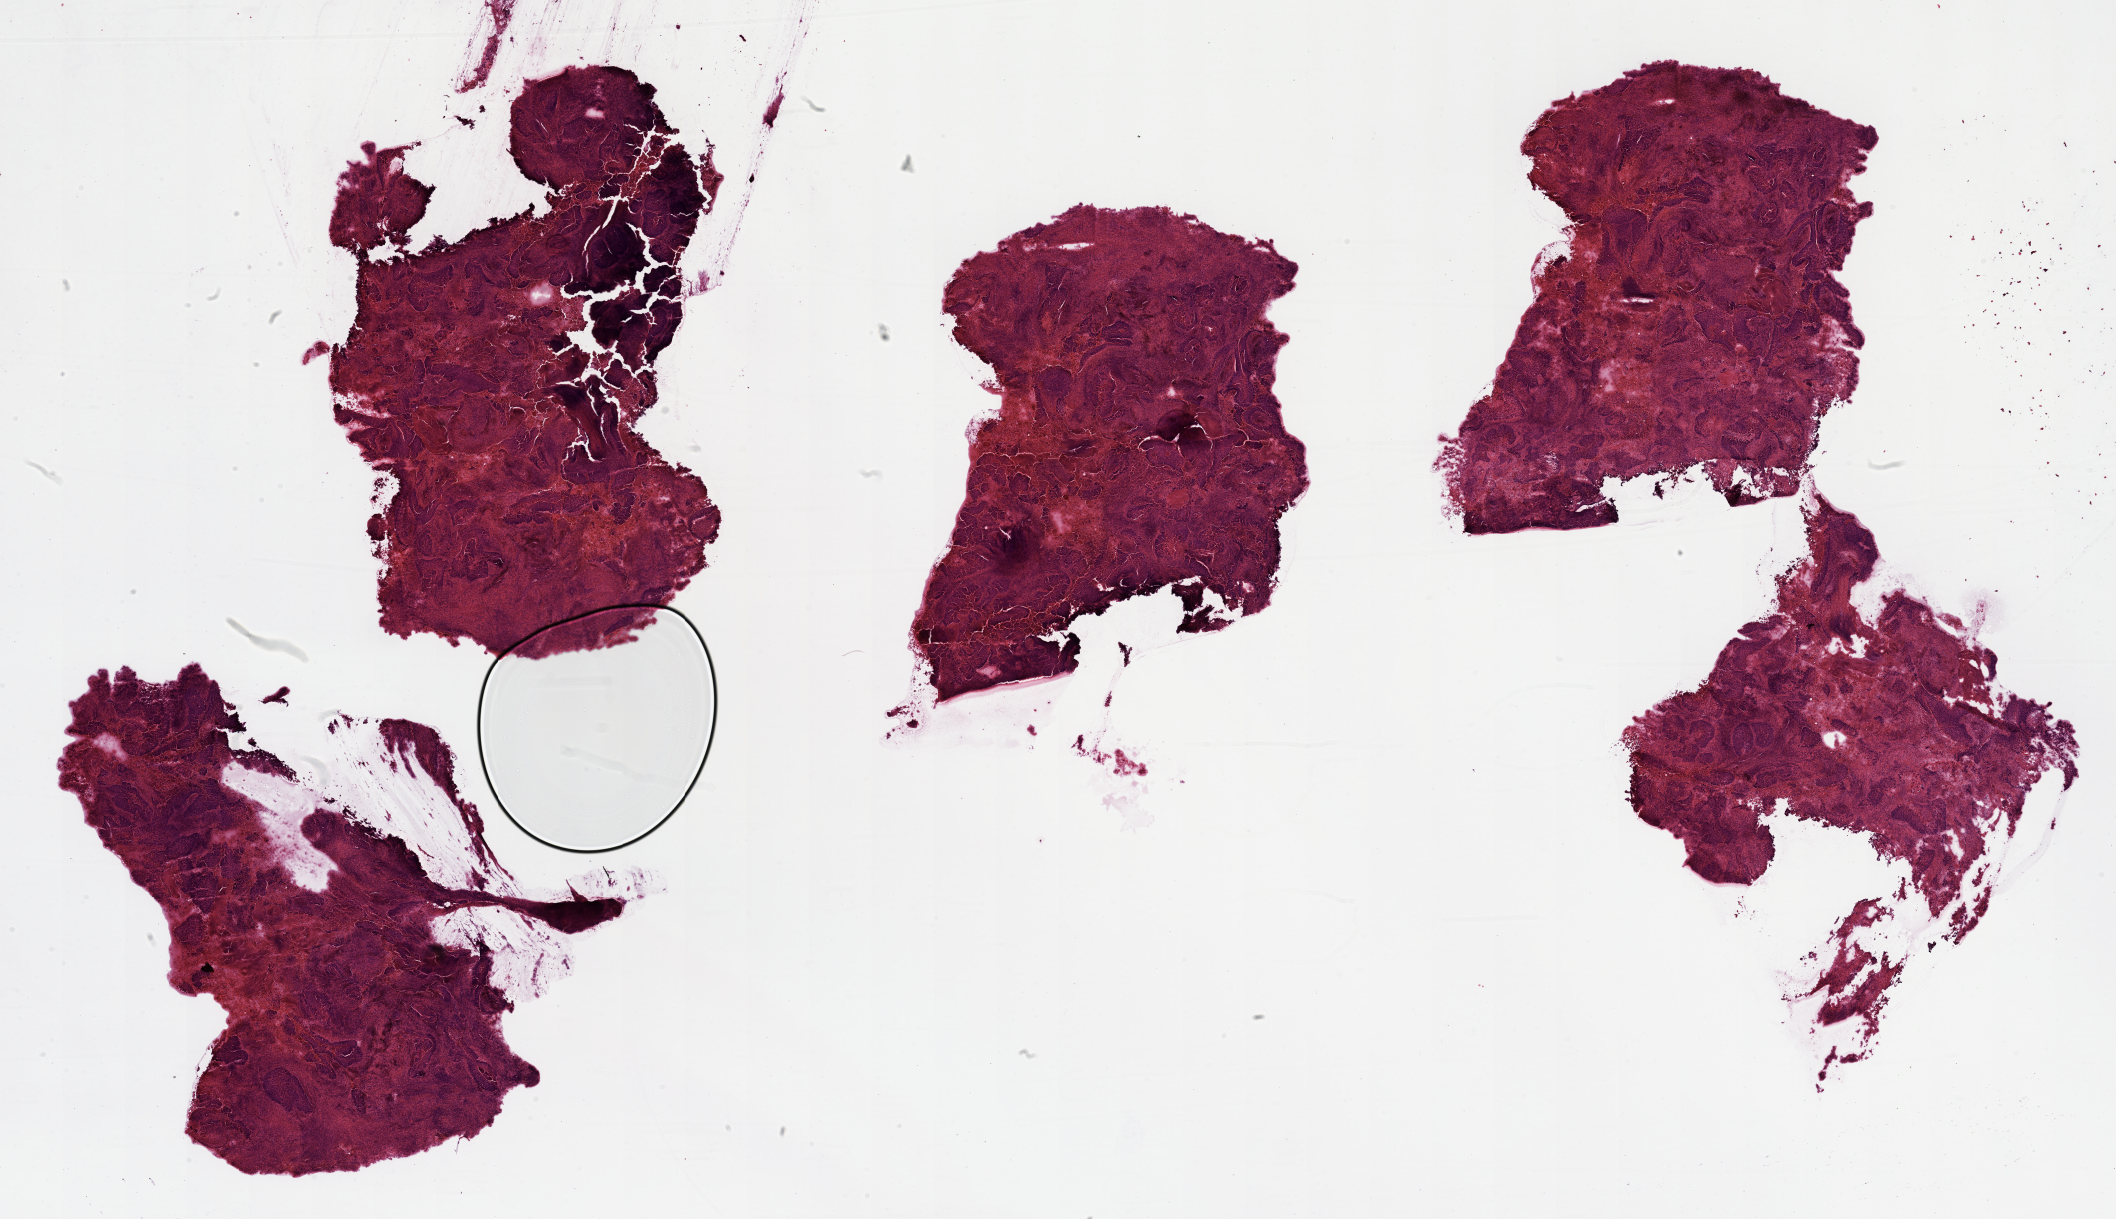
Hematoxylin and eosin (H&E) stained whole-slide image — whole scanned area (about 33.5 x 19.3 mm, from a 20x scan) shown as a low-resolution overview; lung, tumour tissue. 65-year-old male patient.
Primary tumour site (as recorded): left lower lobe. Patient diagnosis (cohort enrolment): squamous cell carcinoma (lung).